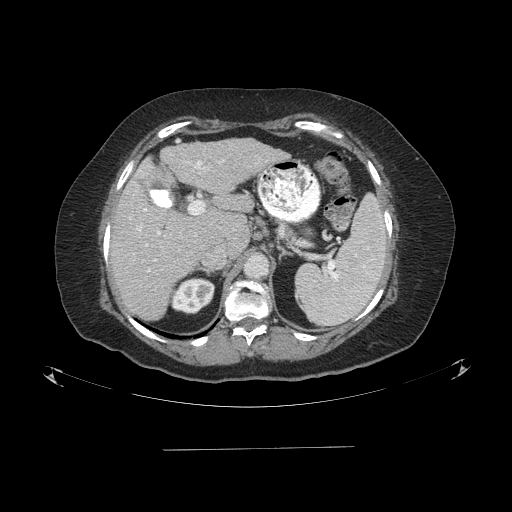
Contrast-enhanced abdominal CT (liver protocol), one axial slice. Position 53 of 103 along the scan axis. Reconstruction kernel STANDARD. 120 kVp. One of 2 acquisitions stored at this slice position. Soft-tissue window (W 400 / L 40 HU). 2.5 mm slice thickness. 512 × 512 image matrix, field of view 500 × 500 mm. Case-level facts recorded for this patient, not image findings: diagnosis: hepatocellular carcinoma (patient treated with transarterial chemoembolisation; whether this scan precedes or follows treatment is not stated here); TNM stage (as recorded): Stage-IIIA; Child-Pugh class: A; tumour differentiation: poorly differentiated; tumour nodularity: multinodular.
Annotated regions visible in this slice (semi-automatically segmented with operator editing):
- liver parenchyma outside the tumour (the mass and vessels are separate outlines, so this box may not span the whole liver): bounding box (x1, y1, x2, y2) in pixels: (110, 138, 288, 320)
- liver vessels: (138, 161, 205, 272)